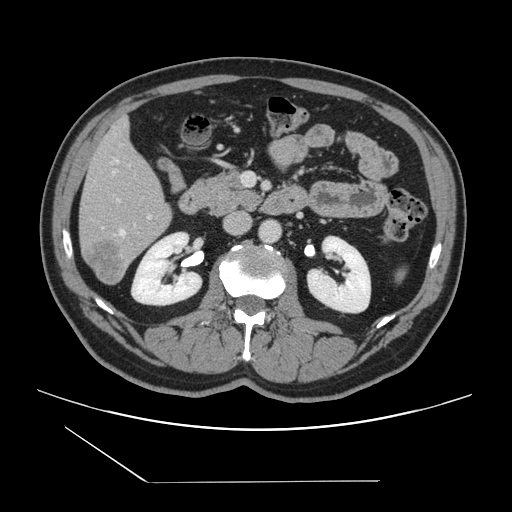
Contrast-enhanced abdominal CT, one axial slice; slice 56 of 157 in the series (ordered by position); 120 kVp; intravenous contrast given; soft-tissue window (W 400 / L 40 HU); 2.5 mm slice thickness; 512 × 512 image matrix, field of view 407 × 407 mm. Male patient, age 61 years. Case-level facts recorded for this patient, not image findings: diagnosis: colorectal cancer liver metastases, imaged before liver resection; multiple liver metastases: yes; largest metastasis: 5.5 cm; disease in both lobes: yes.
Structures marked on this image (outlined manually by an expert reader):
- hepatic veins: bounding box (x1, y1, x2, y2) in pixels: (114, 159, 126, 236)
- liver: (80, 120, 172, 284)
- planned liver remnant (the part of the liver to remain after resection): (81, 121, 167, 218)
- portal vein (with intrahepatic branches): (103, 198, 152, 228)
- liver metastasis: (85, 241, 126, 283)